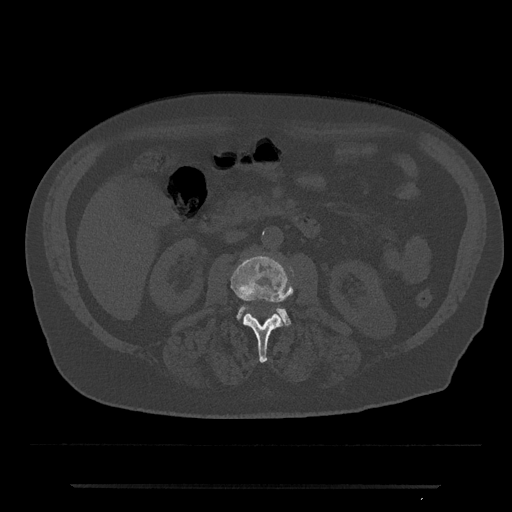
CT including the spine, one axial slice; slice 451 of 797 in the series (ordered by position); reconstruction kernel Br40s/3; bone window (W 1800 / L 400 HU); 0.5 mm slice thickness; 512 × 512 image matrix. Patient: male, 80 years. From the clinical record (not read from this slice): primary cancer: prostate; vertebrae with lytic lesions (as recorded): L1, T11.
Annotated regions visible in this slice (semi-automatically segmented with operator editing):
- L2 vertebra: bounding box [x1, y1, x2, y2] px = [231, 256, 293, 363]
- L3 vertebra: [236, 306, 292, 326]